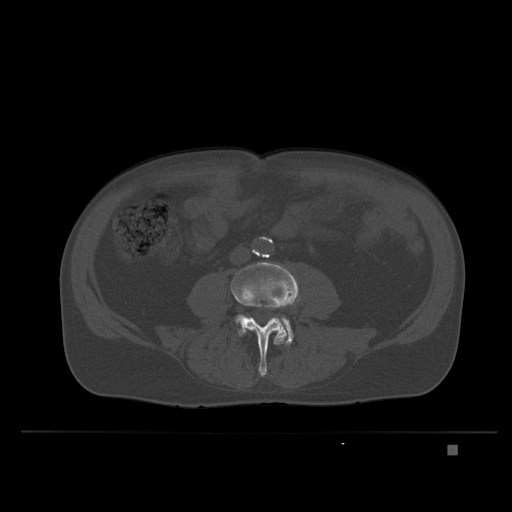
CT including the spine, one axial slice. Slice 72 of 435 in the series (ordered by position). Bone window (W 1800 / L 400 HU). 1.5 mm slice thickness. 512 × 512 image matrix, field of view 434 × 434 mm. Male patient, age 73 years. Case-level facts recorded for this patient, not image findings: primary cancer: skin.
Outlined on this slice (semi-automatically segmented with operator editing):
- L4 vertebra: box from (x=231, y=262) to (x=299, y=377) px
- L5 vertebra: (x=235, y=314)–(x=293, y=345)